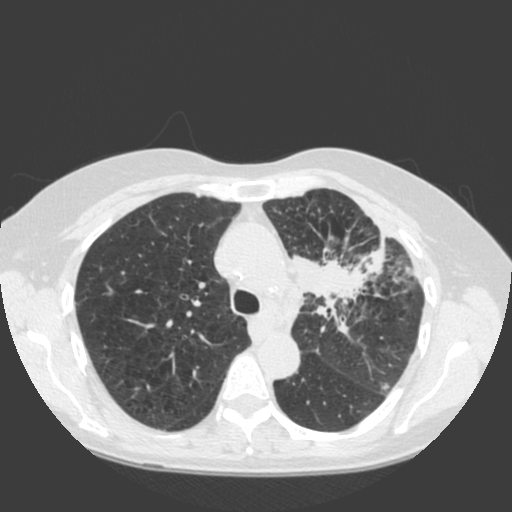
Low-dose screening chest CT, axial slice, baseline annual screen, lung window (W 1500 / L -600 HU), standard (soft-tissue) reconstruction kernel (C), 120 kVp, 512 × 512 image matrix. Female participant, aged 66 years at enrolment. Current smoker at enrolment.
Lesion marked by an expert reader, bounding box (x1, y1, x2, y2) in pixels: (284, 236, 397, 337). Reader record for this screening exam (exam-level; its link to the box is not recorded): non-calcified nodule or mass ≥4 mm, left upper lobe, 61 × 45 mm, spiculated (stellate) margins, soft tissue attenuation. Official screen result: positive, change unspecified: nodule(s) >= 4 mm or enlarging nodule(s), mass(es), or other non-specific abnormalities suspicious for lung cancer. Lung cancer was diagnosed 19 days after this screen: squamous cell carcinoma, keratinizing, NOS, left upper lobe, left hilum, mediastinum, left main stem bronchus, other location, poorly differentiated (G3), stage IIIB (AJCC 6th edition), 60 mm at pathology.